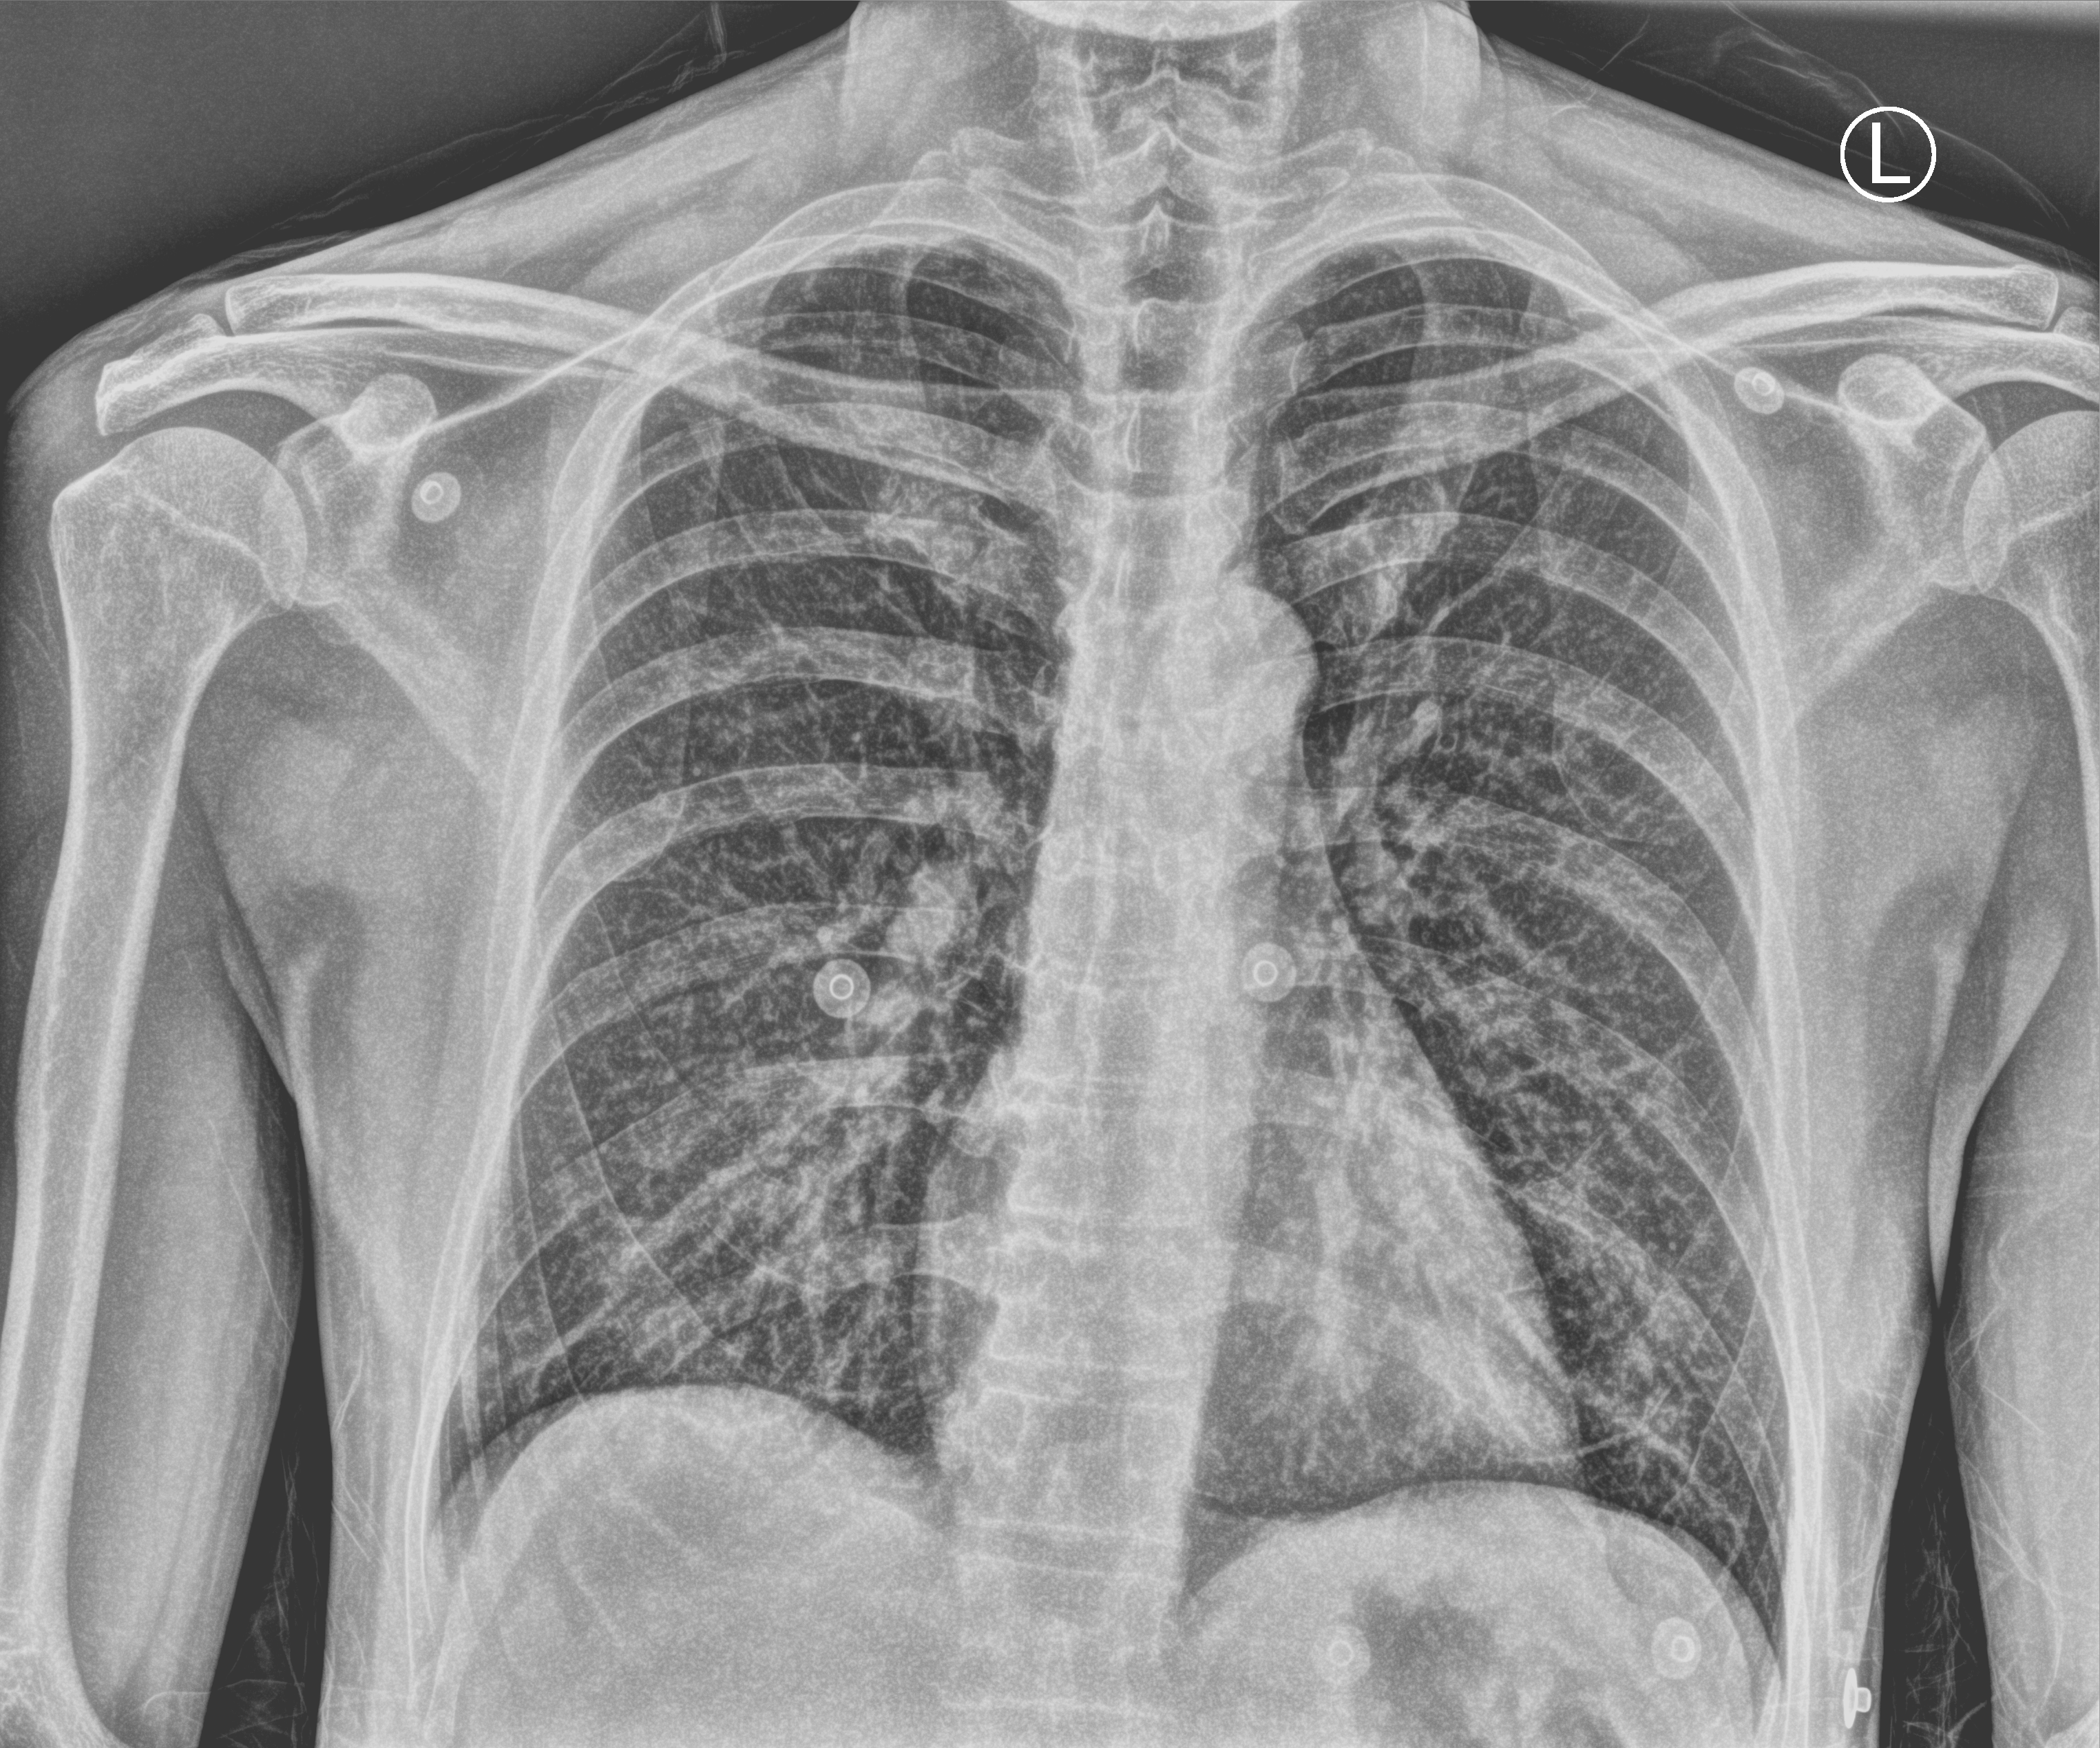
Chest X-ray (portable); anteroposterior (AP) projection. Male patient hospitalised with COVID-19, age 18–59 years.
Hospital-stay facts (about this admission, not read from this image; timing relative to this image not recorded): mechanically ventilated during this hospital stay: no; length of hospital stay: 1 day; admitted to intensive care during this hospital stay: no.